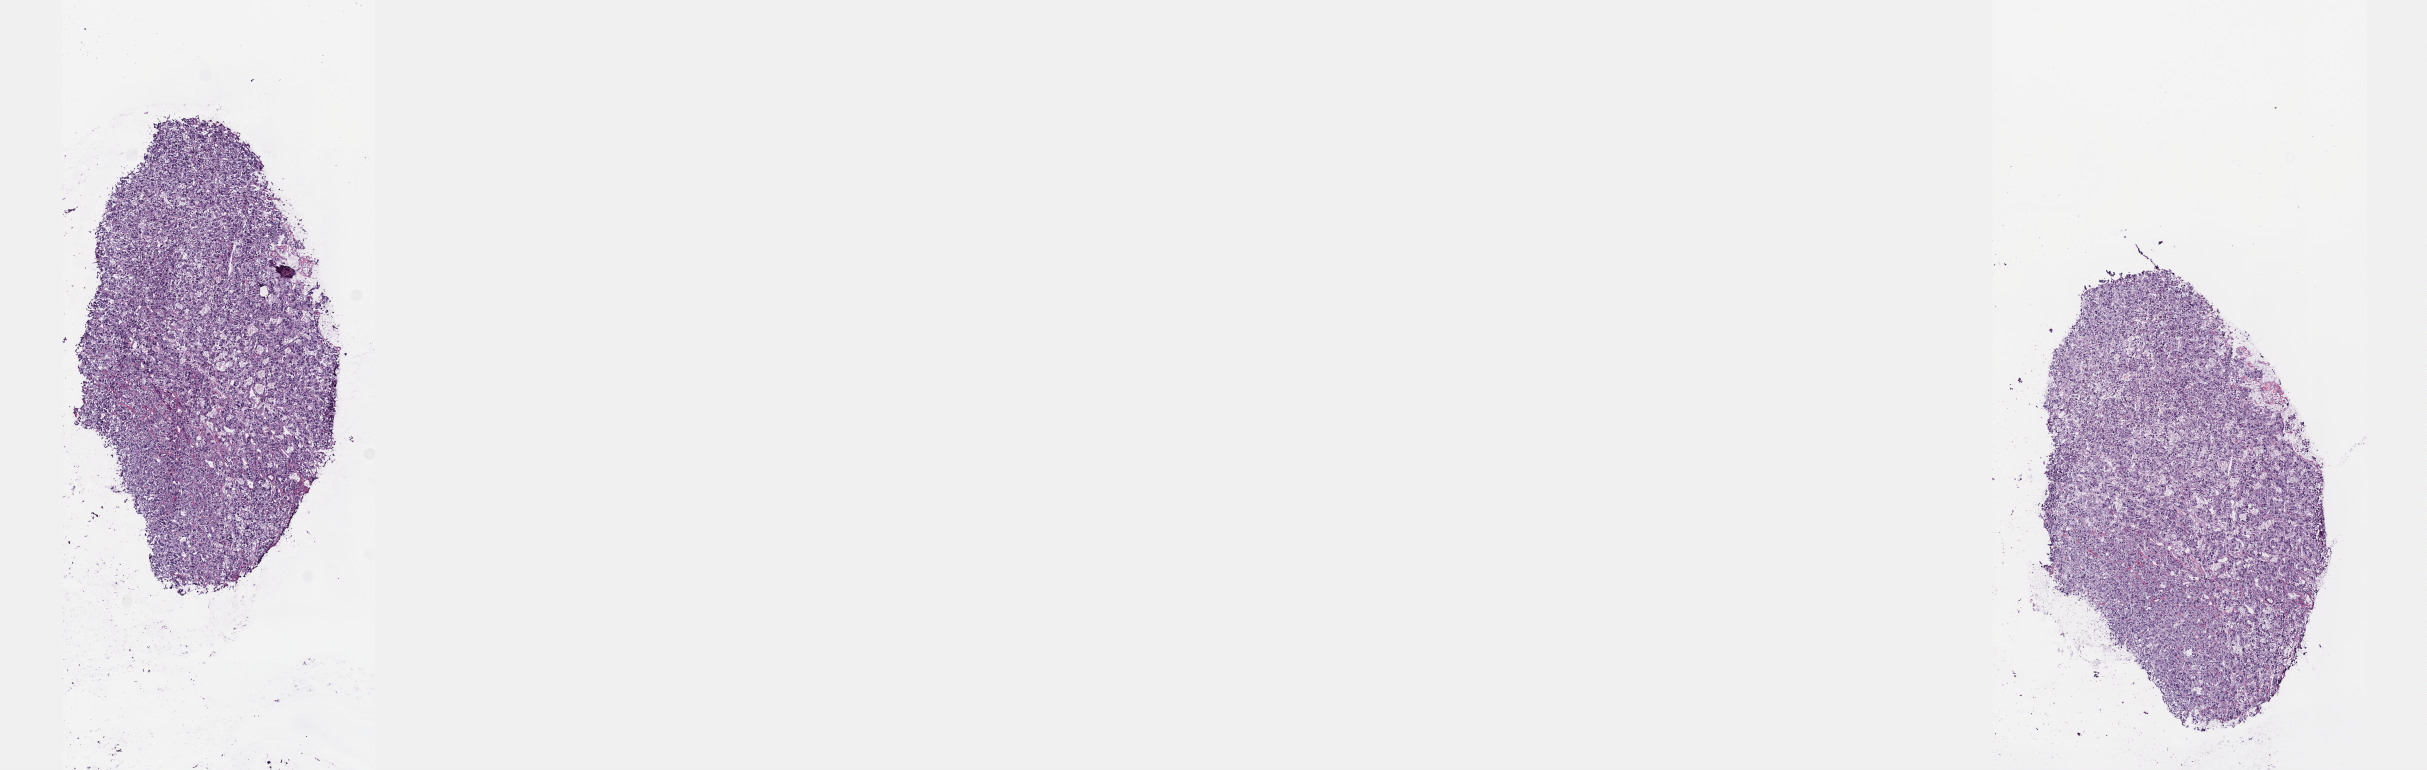
Hematoxylin and eosin (H&E) stained whole-slide image, low-resolution overview of the scanned area, about 19.6 x 6.2 mm (acquisition: 40x scan), frozen section from the top of the tissue portion, sample: primary tumour, adrenal gland. Female patient; age at initial diagnosis 82 years. Slide review estimates, as recorded: tumour cells 85%, tumour nuclei 85%, normal cells 0%, stromal cells 15%, necrosis 0%. Infiltration values recorded for this section: lymphocyte infiltration 0%, monocyte infiltration 0%, neutrophil infiltration 0%.
Diagnosis: Pheochromocytoma, NOS.